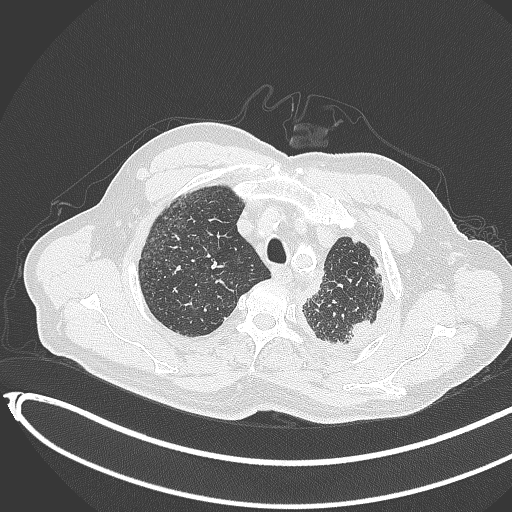
Chest CT, one axial slice. Position 362 of 451 along the scan axis. Reconstruction kernel B70f. Lung window (W 1500 / L -600 HU). 1 mm slice thickness. 512 × 512 image matrix, field of view 400 × 400 mm. Male patient, age 78 years. From the clinical record (not read from this slice): clinical TNM (as recorded): T1c N0 M1.
Outlined on this slice (rectangle marked by the reading radiologist):
- lung tumour (recorded histology: adenocarcinoma): bounding box [x1, y1, x2, y2] px = [346, 315, 376, 345]